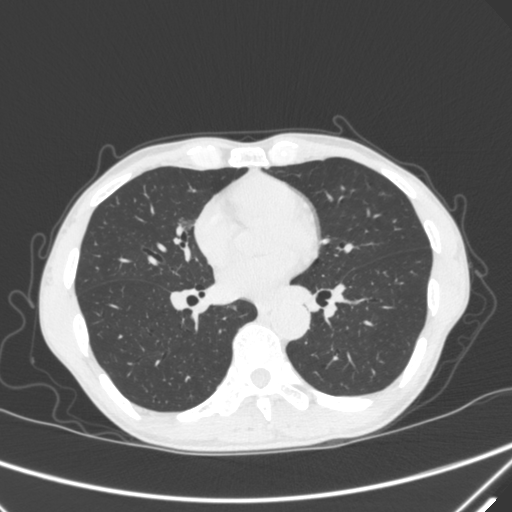
Chest CT, one axial slice. Position 159 of 340 along the scan axis. Lung window (W 1500 / L -600 HU). 512 × 512 image matrix, field of view 350 × 350 mm. Patient: male, 67 years. Case-level facts recorded for this patient, not image findings: clinical TNM (as recorded): T1c N0 M0.
Outlined on this slice (bounding box drawn by a radiologist):
- lung tumour (recorded histology: adenocarcinoma): bounding box <172,203,201,235> (left, top, right, bottom; pixels)